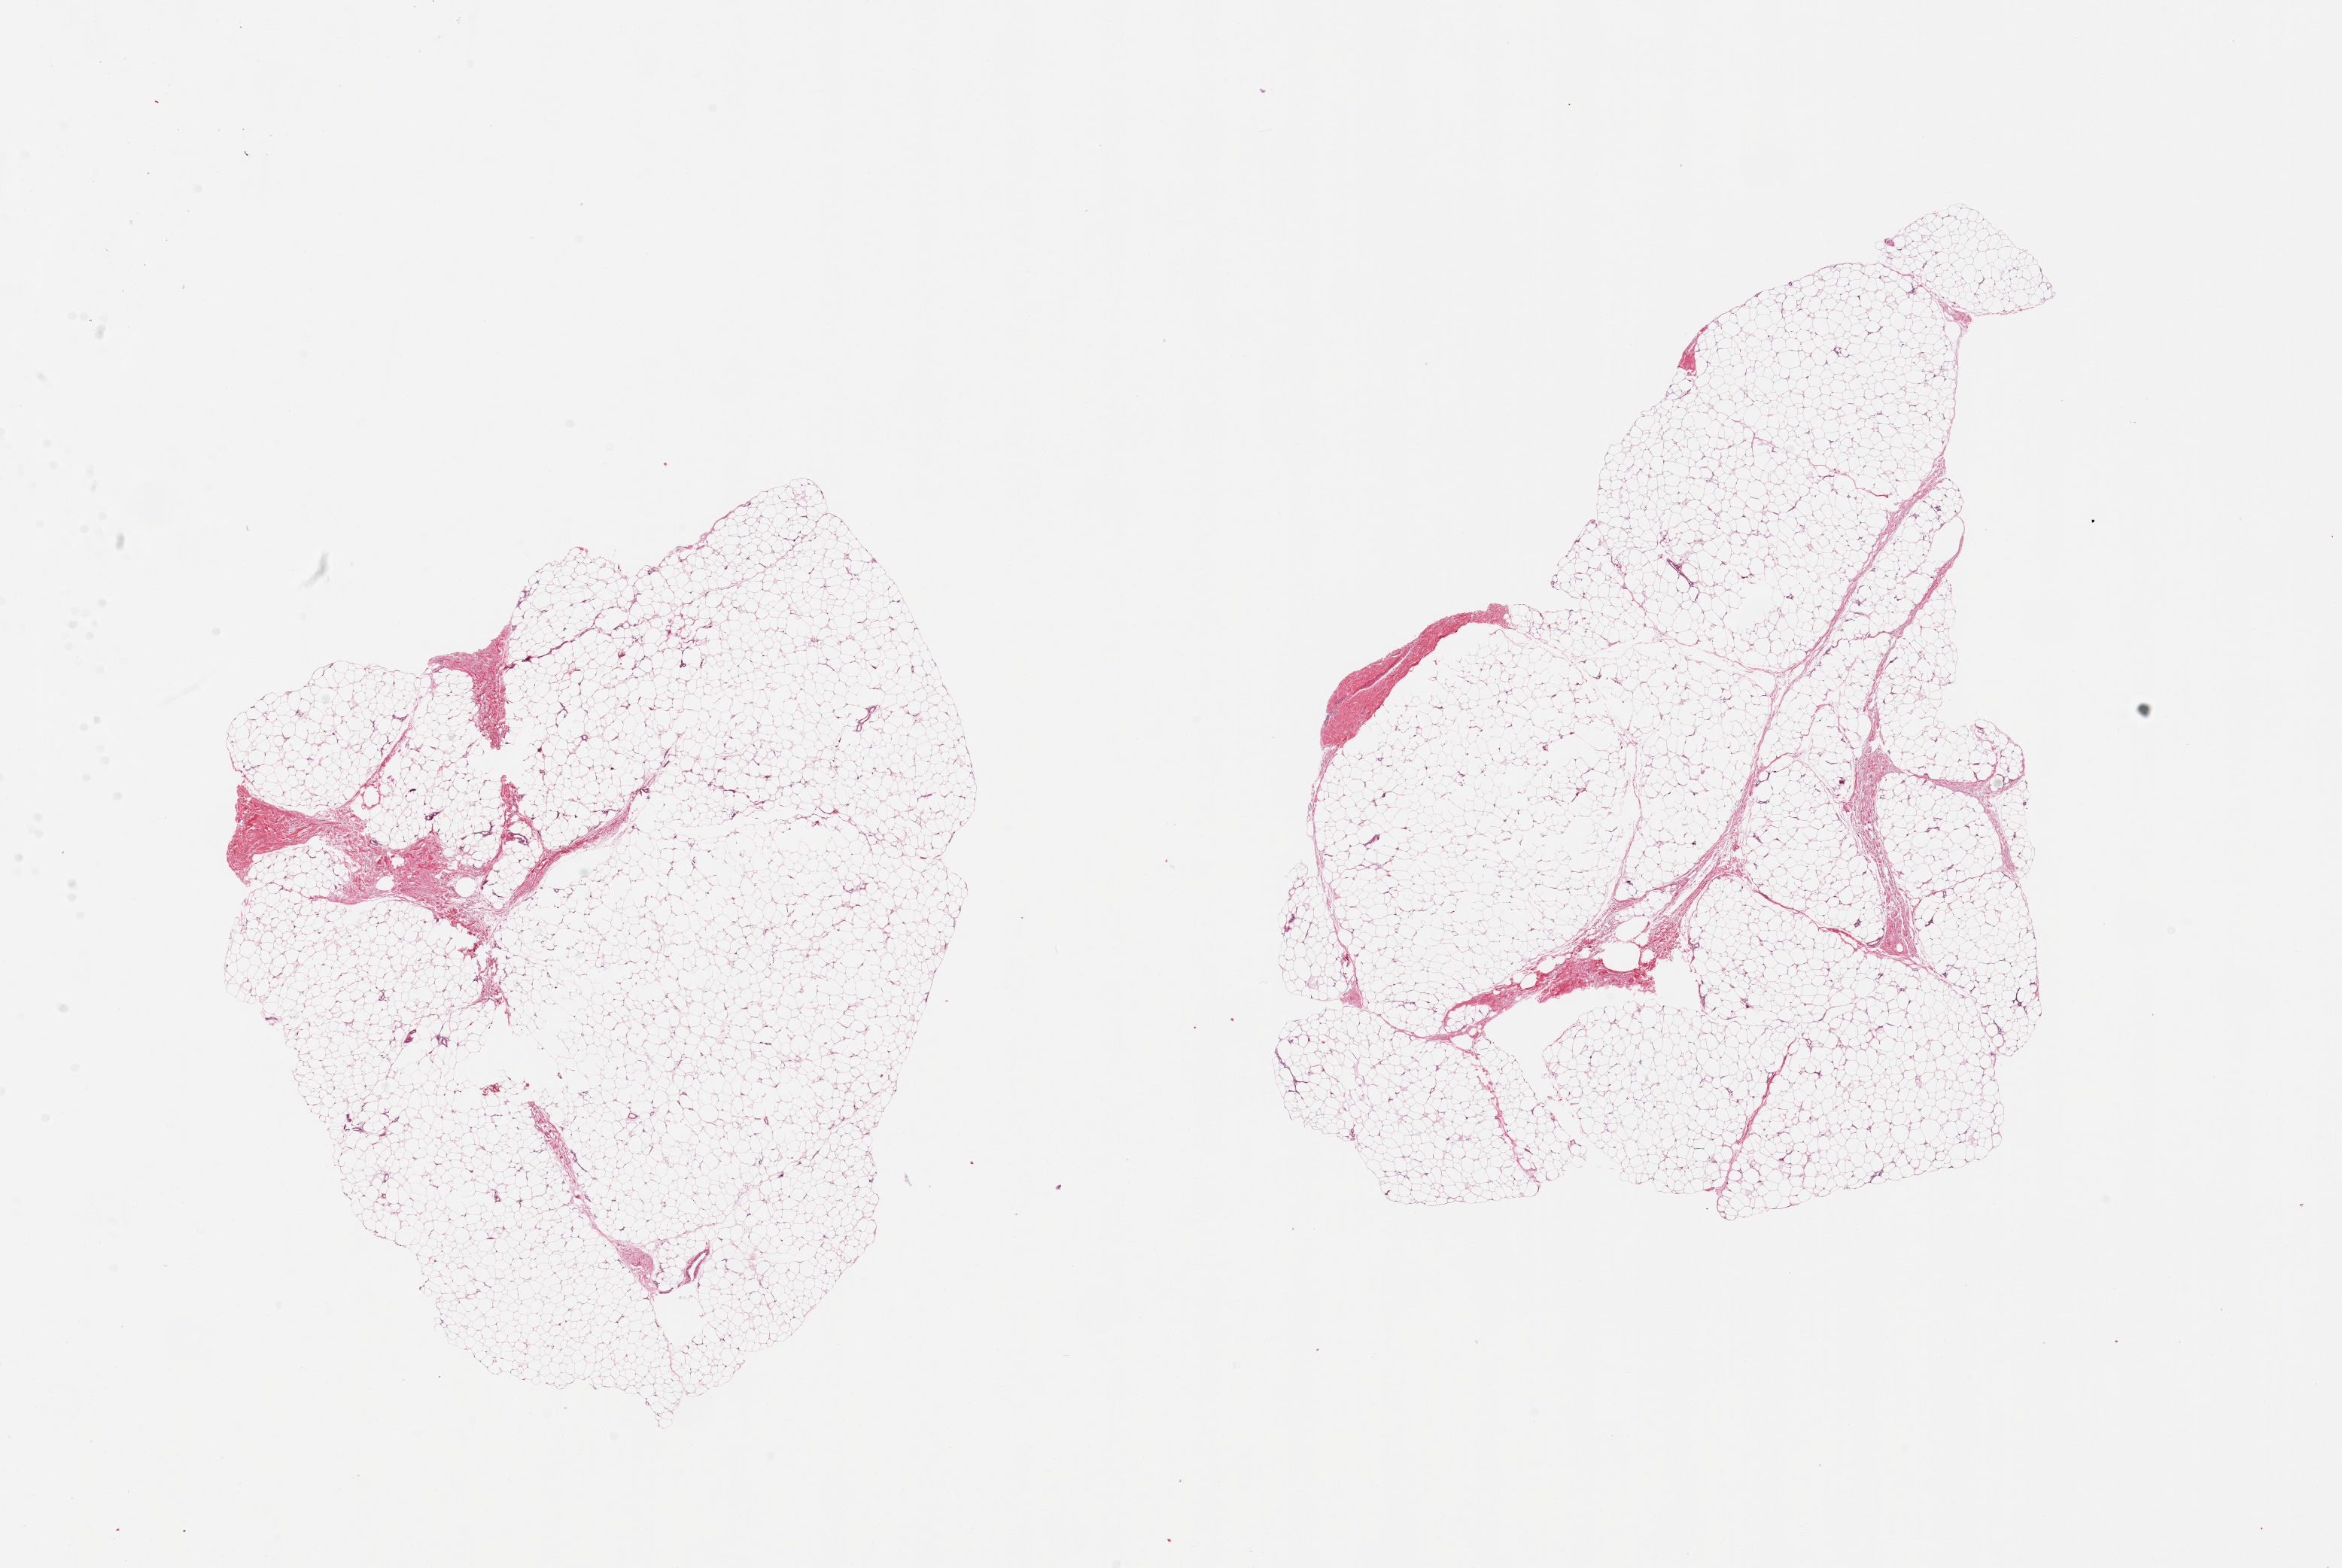
Whole-slide image, hematoxylin and eosin (H&E) stain — a low-resolution overview of the entire scanned area, about 24.6 x 16.5 mm (from a 20x scan), PAXgene-fixed paraffin-embedded (PFPE) section, section of adipose tissue (target tissue), tissue donor sample. Male donor.
Pathologist's review note for this sample: 2 pieces, ~10% fascia.